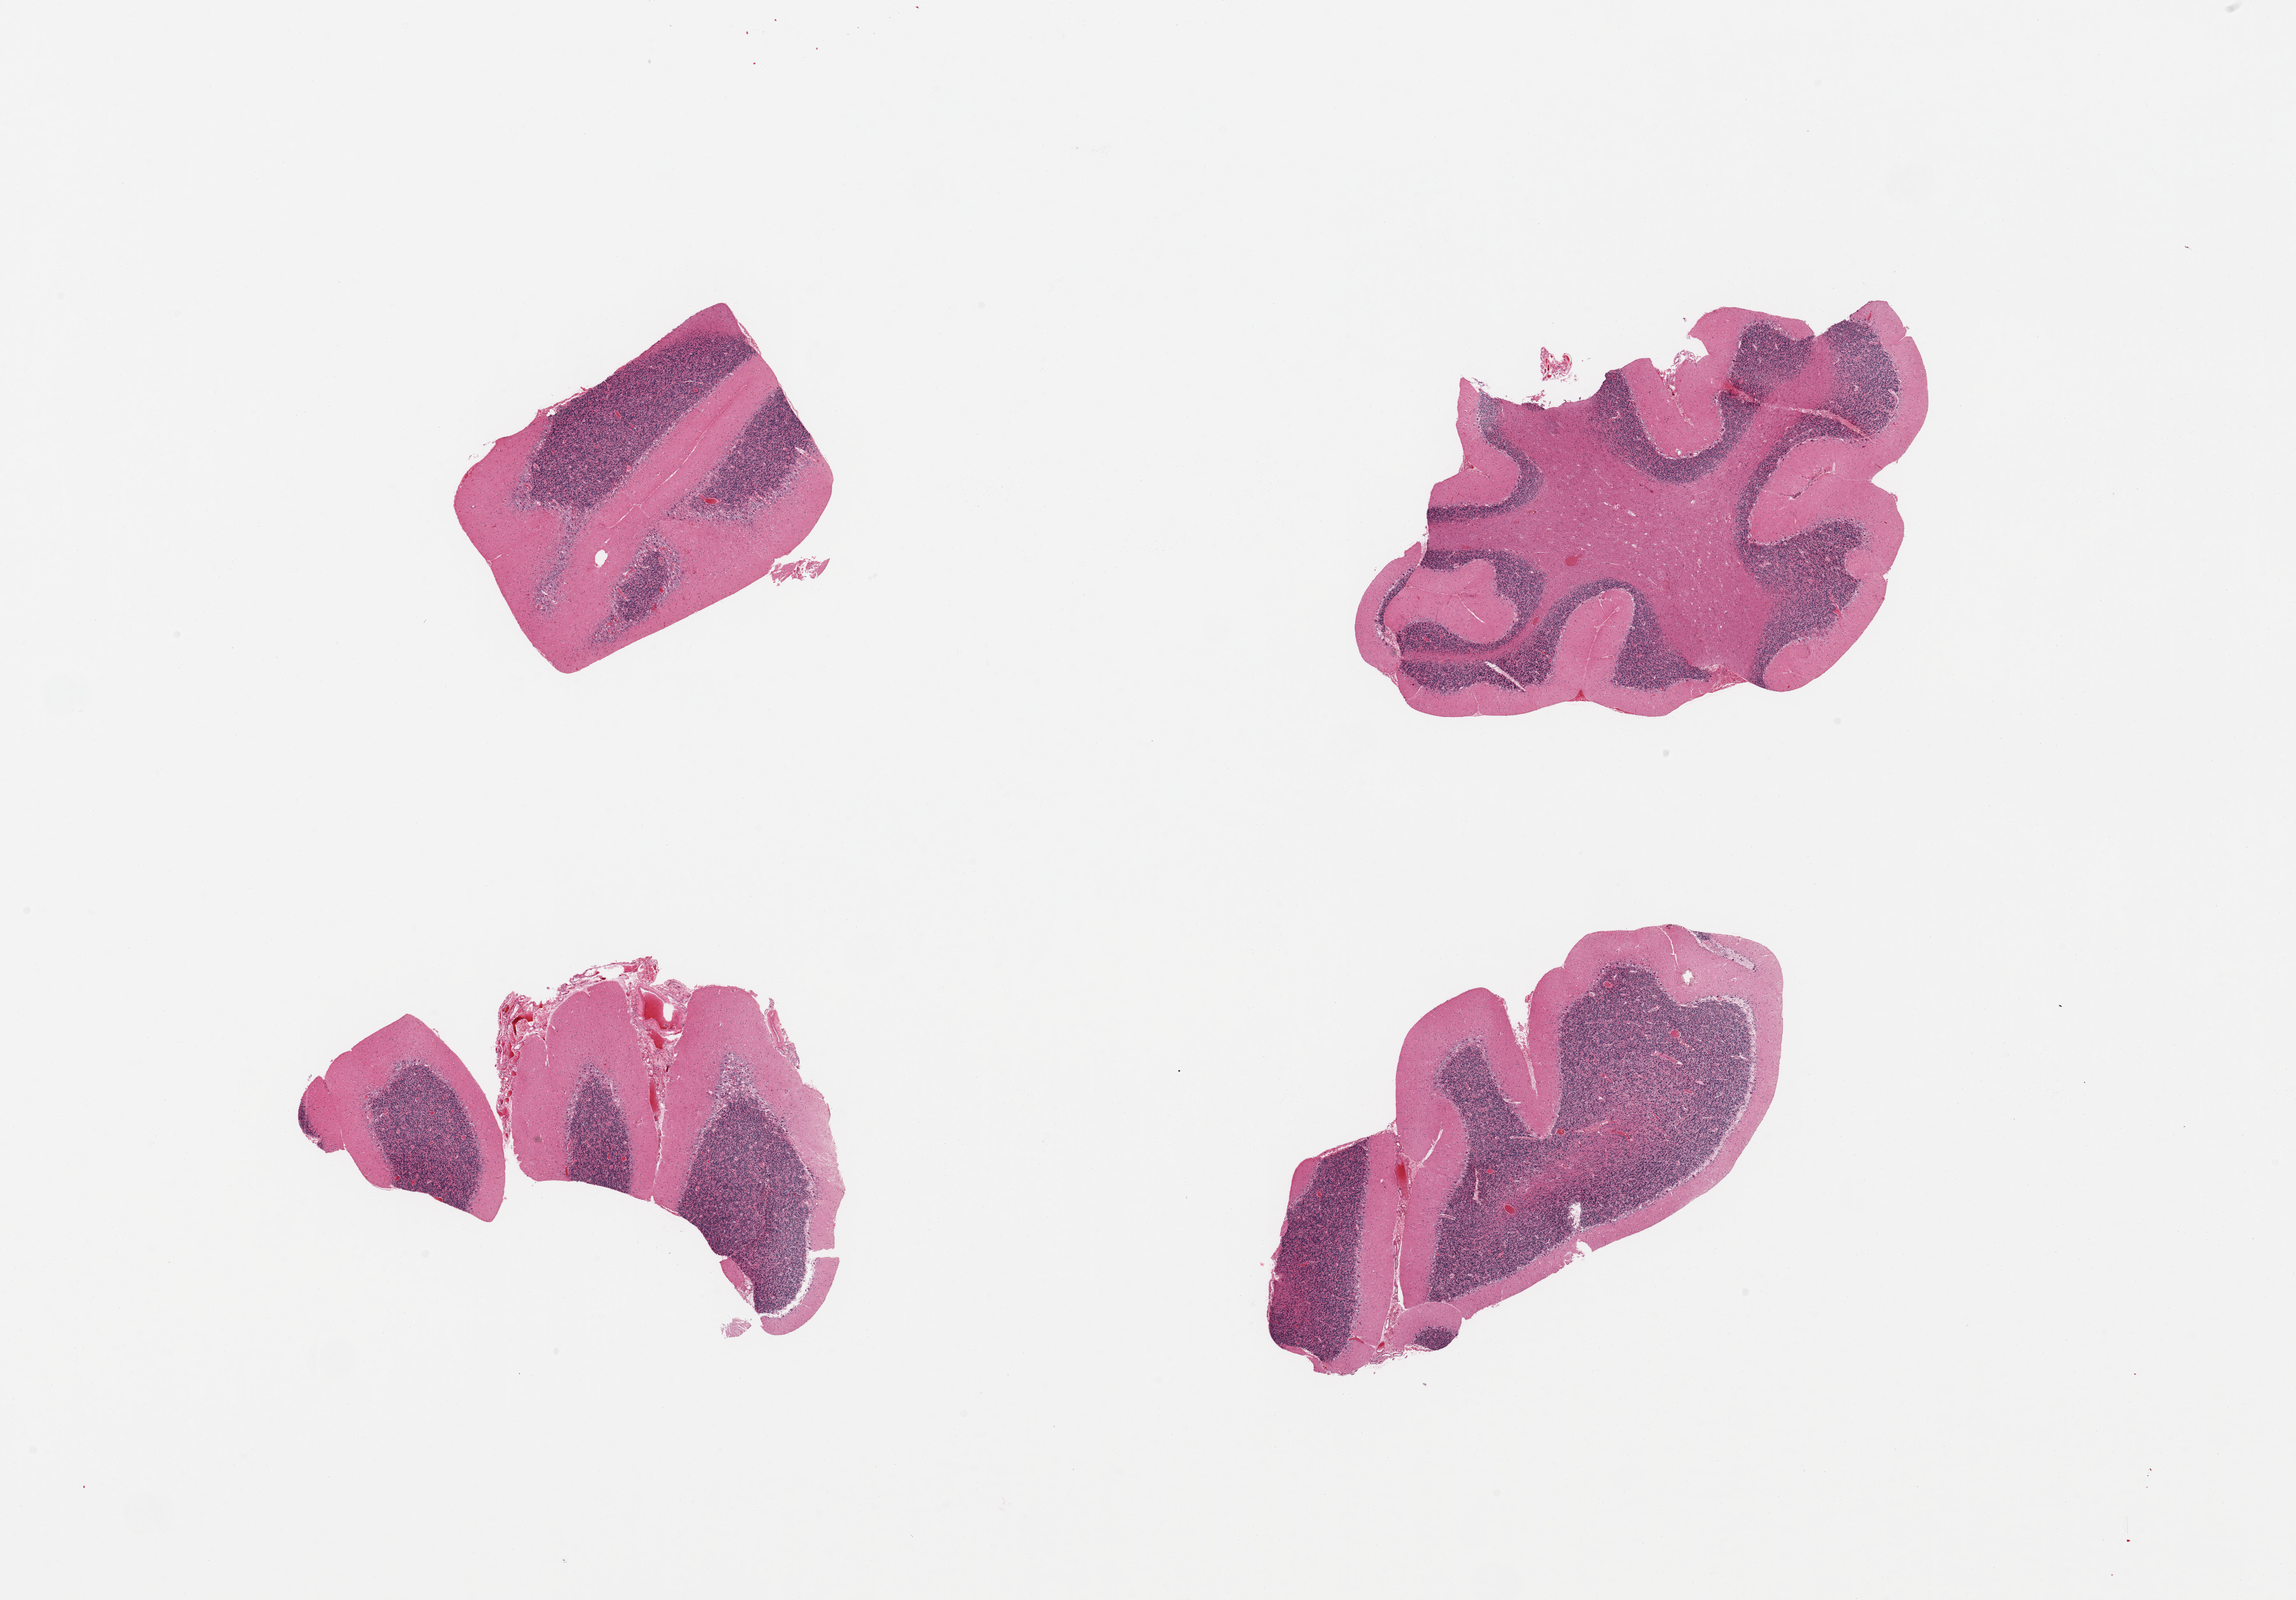
Whole-slide image, hematoxylin and eosin (H&E) stain, a low-resolution overview of the entire scanned area, about 28.5 x 19.9 mm (slide scanned at 20x), PAXgene-fixed, paraffin-embedded tissue, target tissue: cerebellum, tissue donor sample. Donor sex: male.
* reviewer comment on this tissue sample: 2 pieces, no abnormalities